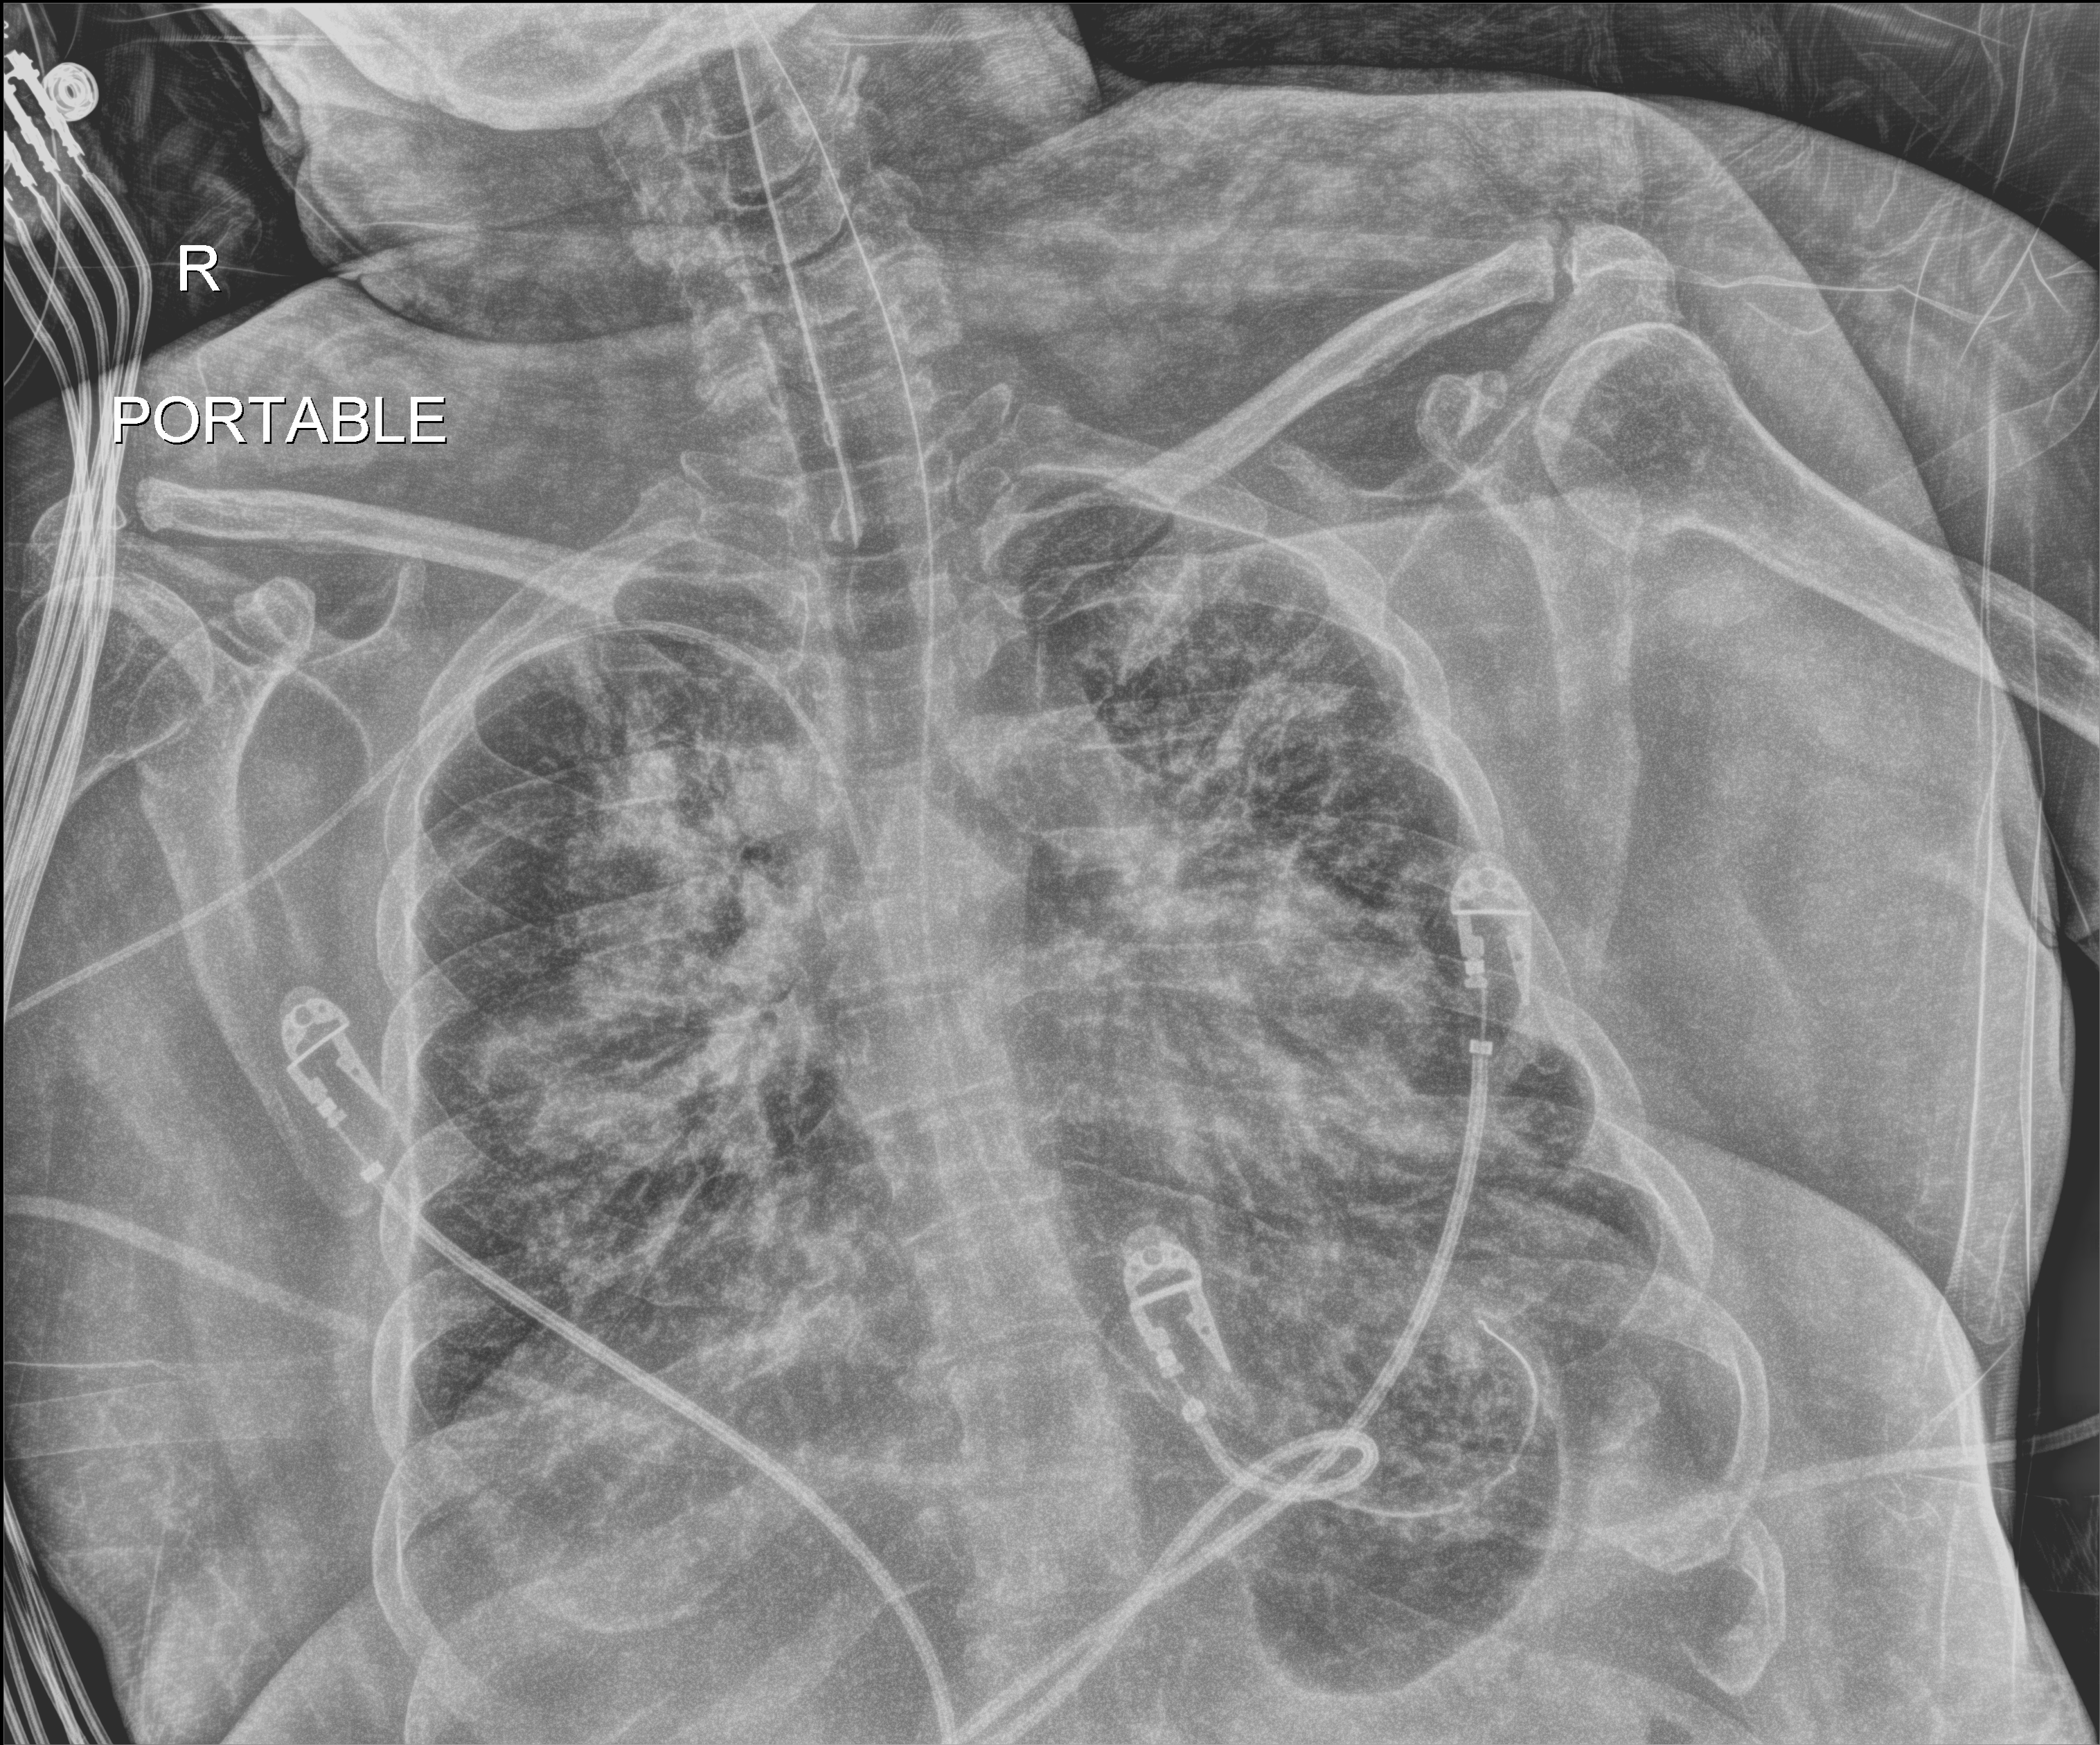
Chest radiograph, anteroposterior (AP) projection. Adult patient hospitalised with COVID-19, age 18–59 years.
From the hospital-stay record, not from the radiograph (when in the stay this image was taken is not recorded): admitted to intensive care during this hospital stay: yes; mechanically ventilated during this hospital stay: yes.